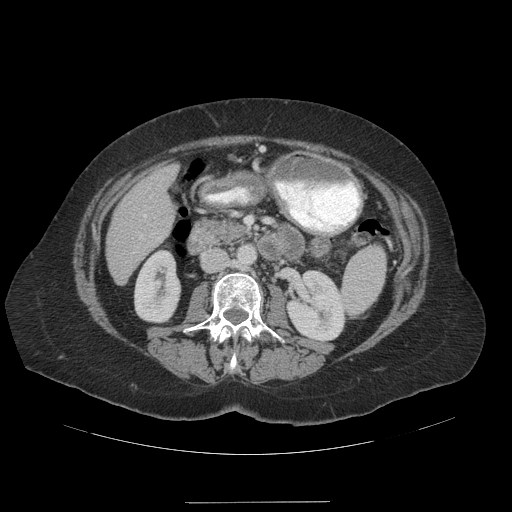
Contrast-enhanced abdominal CT (liver protocol), one axial slice; reconstruction kernel STANDARD; 140 kVp; soft-tissue window (W 400 / L 40 HU); 2.5 mm slice thickness; 512 × 512 image matrix. Case-level facts recorded for this patient, not image findings: diagnosis: hepatocellular carcinoma (patient treated with transarterial chemoembolisation; whether this scan precedes or follows treatment is not stated here); TNM stage (as recorded): Stage-IVA; Child-Pugh class: A; tumour nodularity: multinodular.
Annotated regions visible in this slice (semi-automatic segmentation, software-assisted and operator-edited):
- liver parenchyma outside the tumour (the mass and vessels are separate outlines, so this box may not span the whole liver): bounding box <106,166,176,284> (left, top, right, bottom; pixels)
- liver vessels: <143,214,147,218>